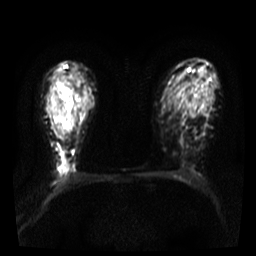
Breast MRI, one axial slice. Slice 24 of 36 in the series (ordered by position). Diffusion-weighted series; image 2 of 4 stored at this slice position (different b-values; order by instance number). 3 T. 5 mm slice thickness. 256 × 256 image matrix, field of view 300 × 300 mm. Female patient.
Annotated regions visible in this slice (outlined manually by an expert reader):
- tumour on diffusion-weighted imaging: bounding box [x1, y1, x2, y2] px = [55, 103, 64, 113]